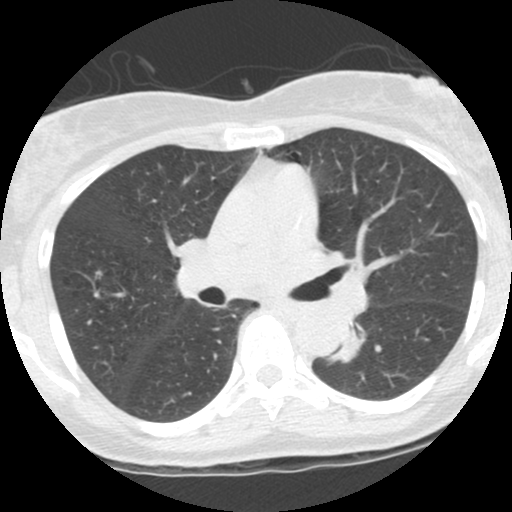
Low-dose screening chest CT, one axial slice. Reconstruction kernel STANDARD. 120 kVp. Lung window (W 1500 / L -600 HU). 512 × 512 image matrix.
Structures marked on this image (manually delineated by an expert):
- lesion 1 (tumor, lower lobe of left lung): bounding box <331,333,361,362> (left, top, right, bottom; pixels)